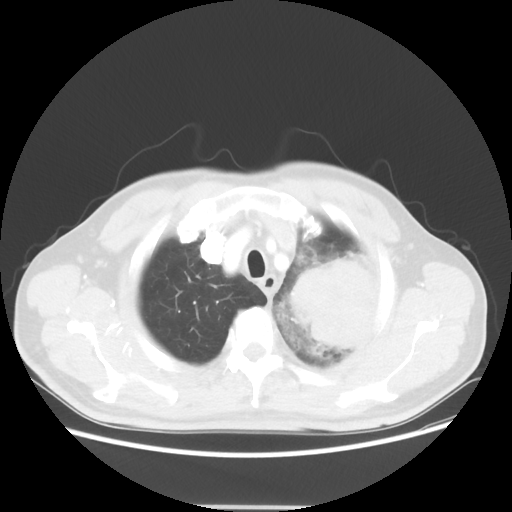
Chest CT, one axial slice. Slice 47 of 53 in the series (ordered by position). Lung window (W 1500 / L -600 HU). 5 mm slice thickness. 512 × 512 image matrix, field of view 391 × 391 mm. Patient: male, 60 years. Case-level facts recorded for this patient, not image findings: clinical TNM (as recorded): T4 N1 M1a.
Outlined on this slice (rectangle marked by the reading radiologist):
- lung tumour (recorded histology: large cell carcinoma): box from (x=283, y=252) to (x=384, y=356) px